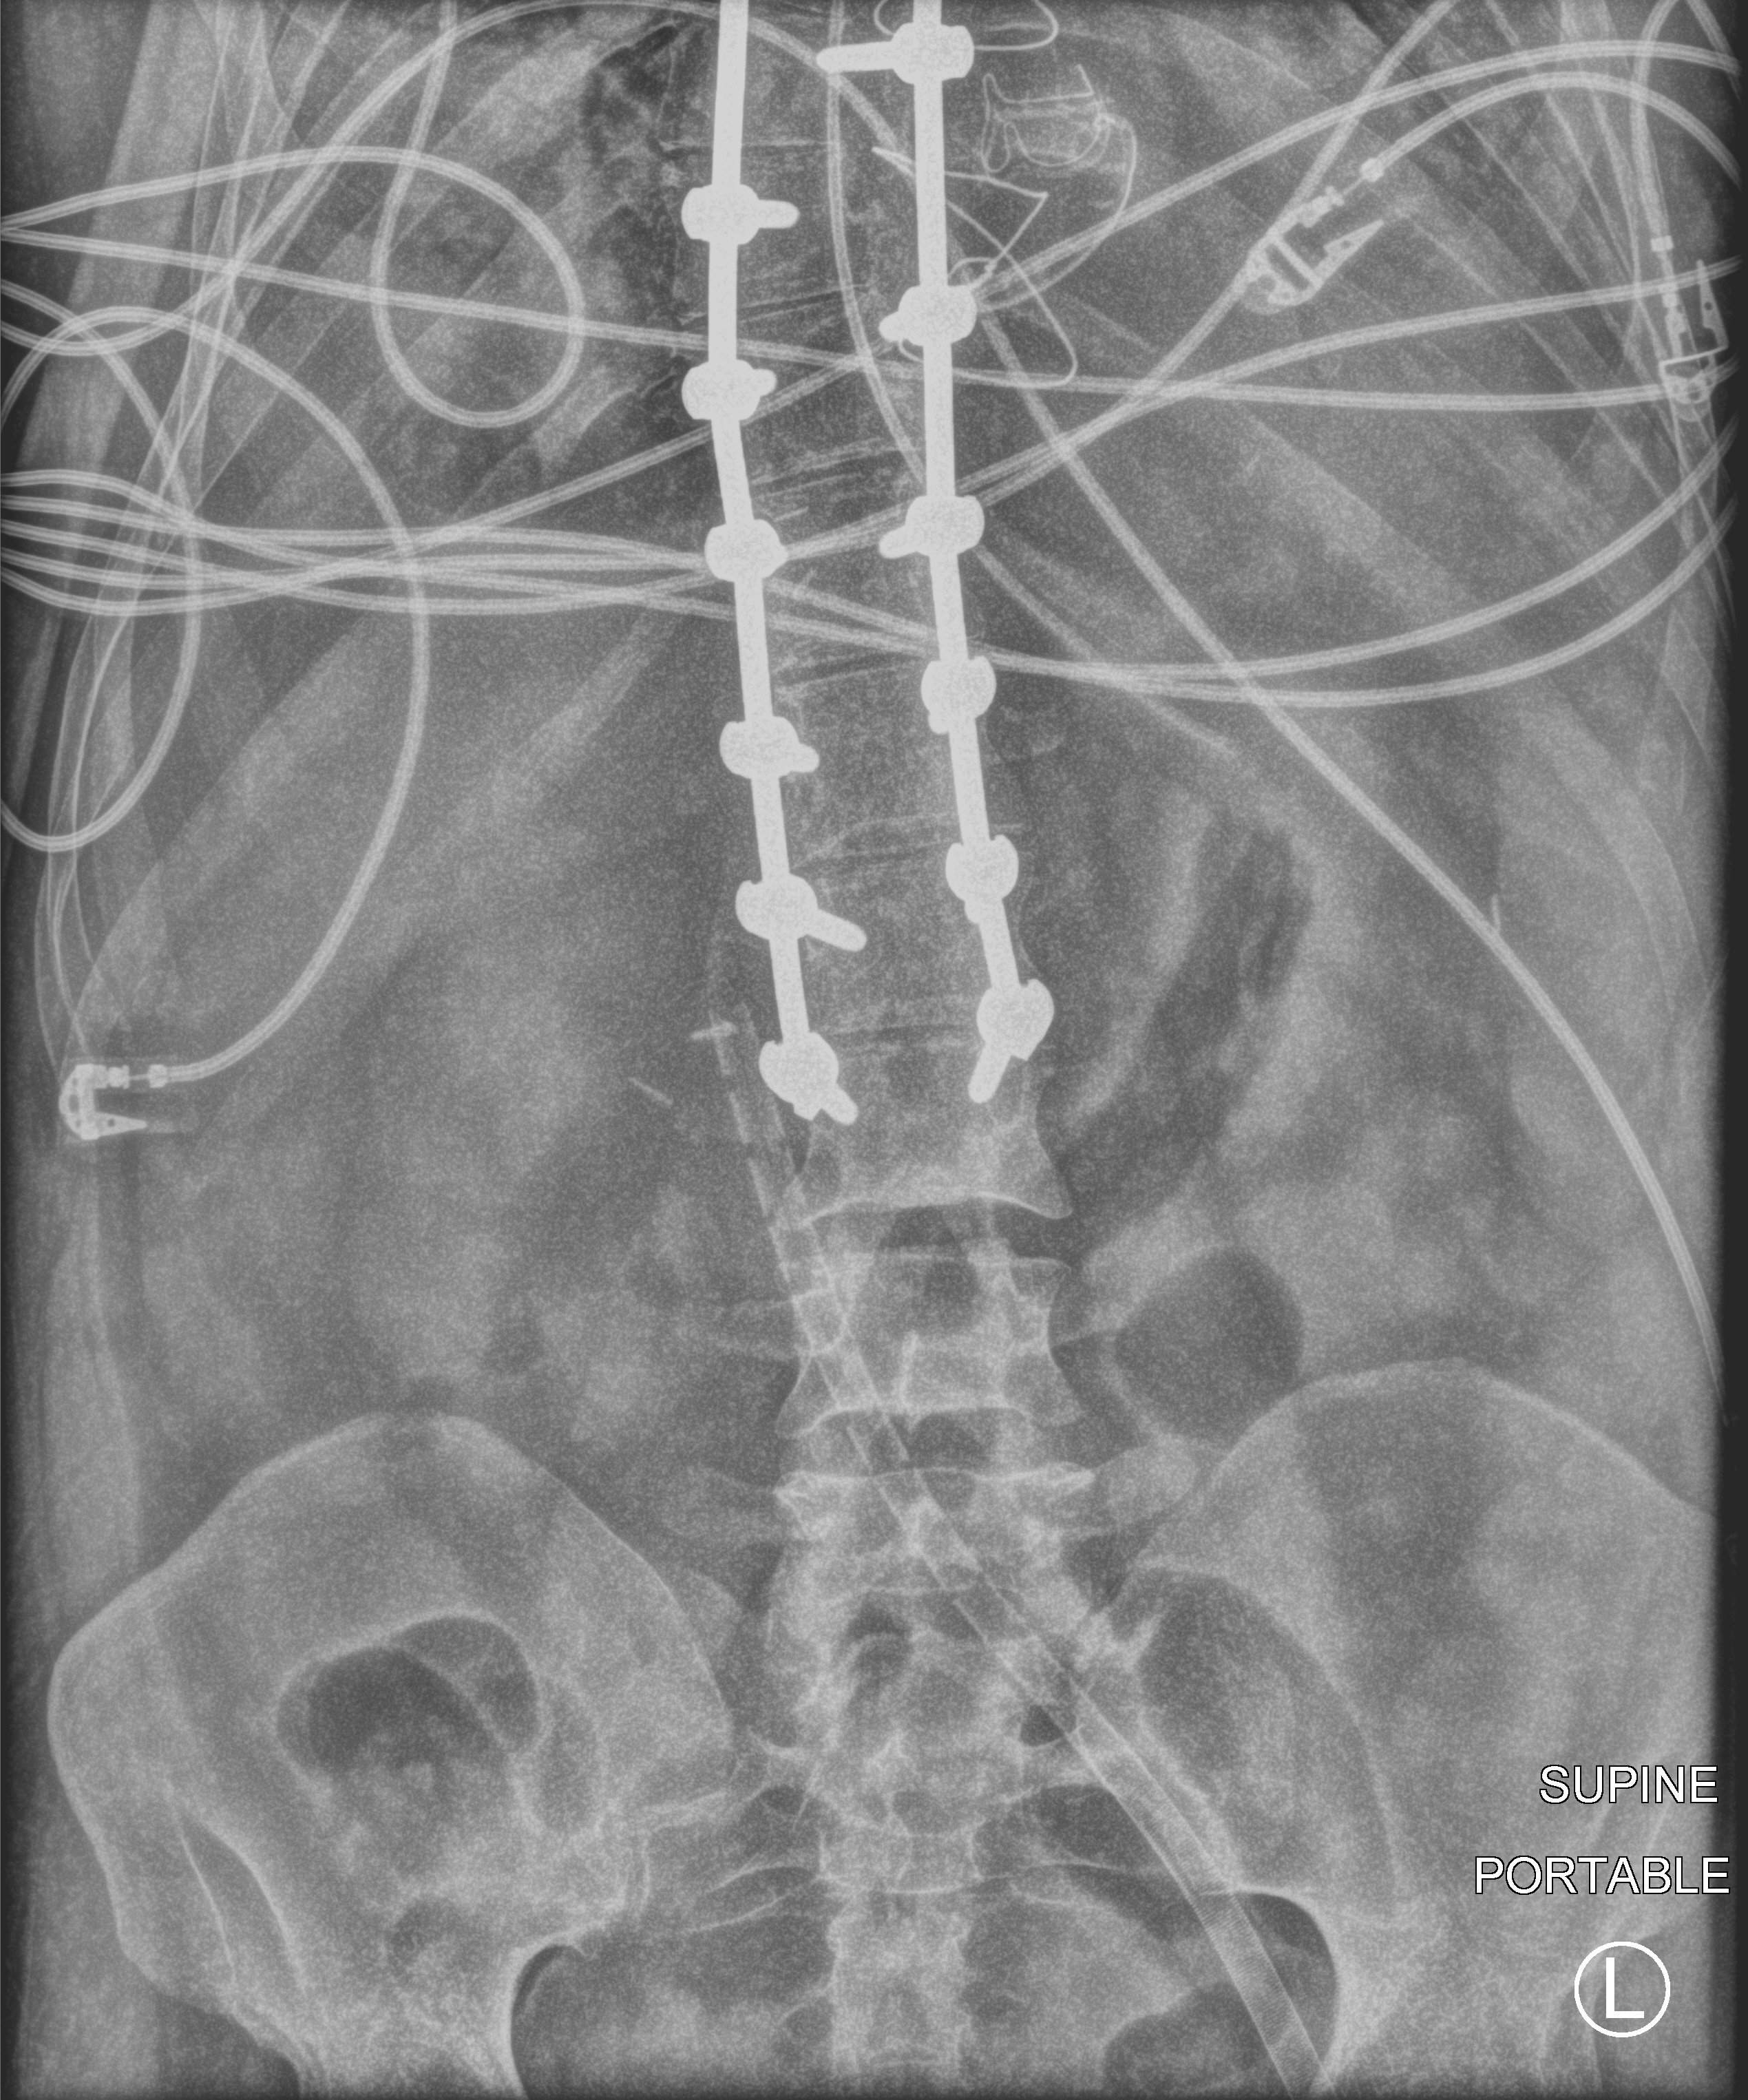
Abdomen X-ray (portable). Patient hospitalised with COVID-19, aged 18–59 years.
Admission-level facts for this patient (not findings on this image; timing relative to this image not recorded): mechanically ventilated during this hospital stay: yes.